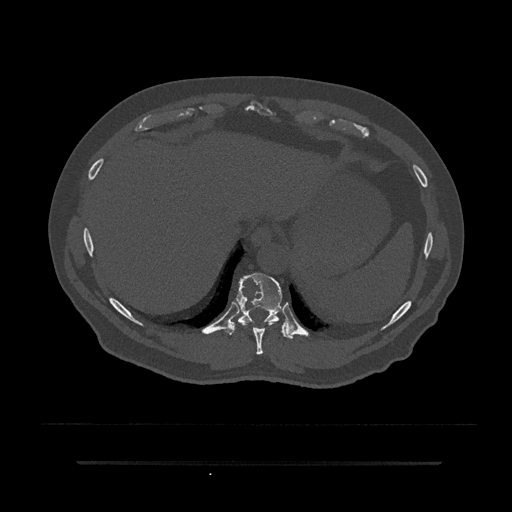
CT including the spine, one axial slice; reconstruction kernel Br40s/3; 120 kVp; bone window (W 1800 / L 400 HU); 0.5 mm slice thickness; 512 × 512 image matrix, field of view 464 × 464 mm. Patient: male, 59 years. From the clinical record (not read from this slice): primary cancer: bile ducts.
Structures marked on this image (semi-automatic segmentation, software-assisted and operator-edited):
- T10 vertebra: box from (x=226, y=273) to (x=294, y=339) px
- T9 vertebra: (x=243, y=323)–(x=272, y=355)